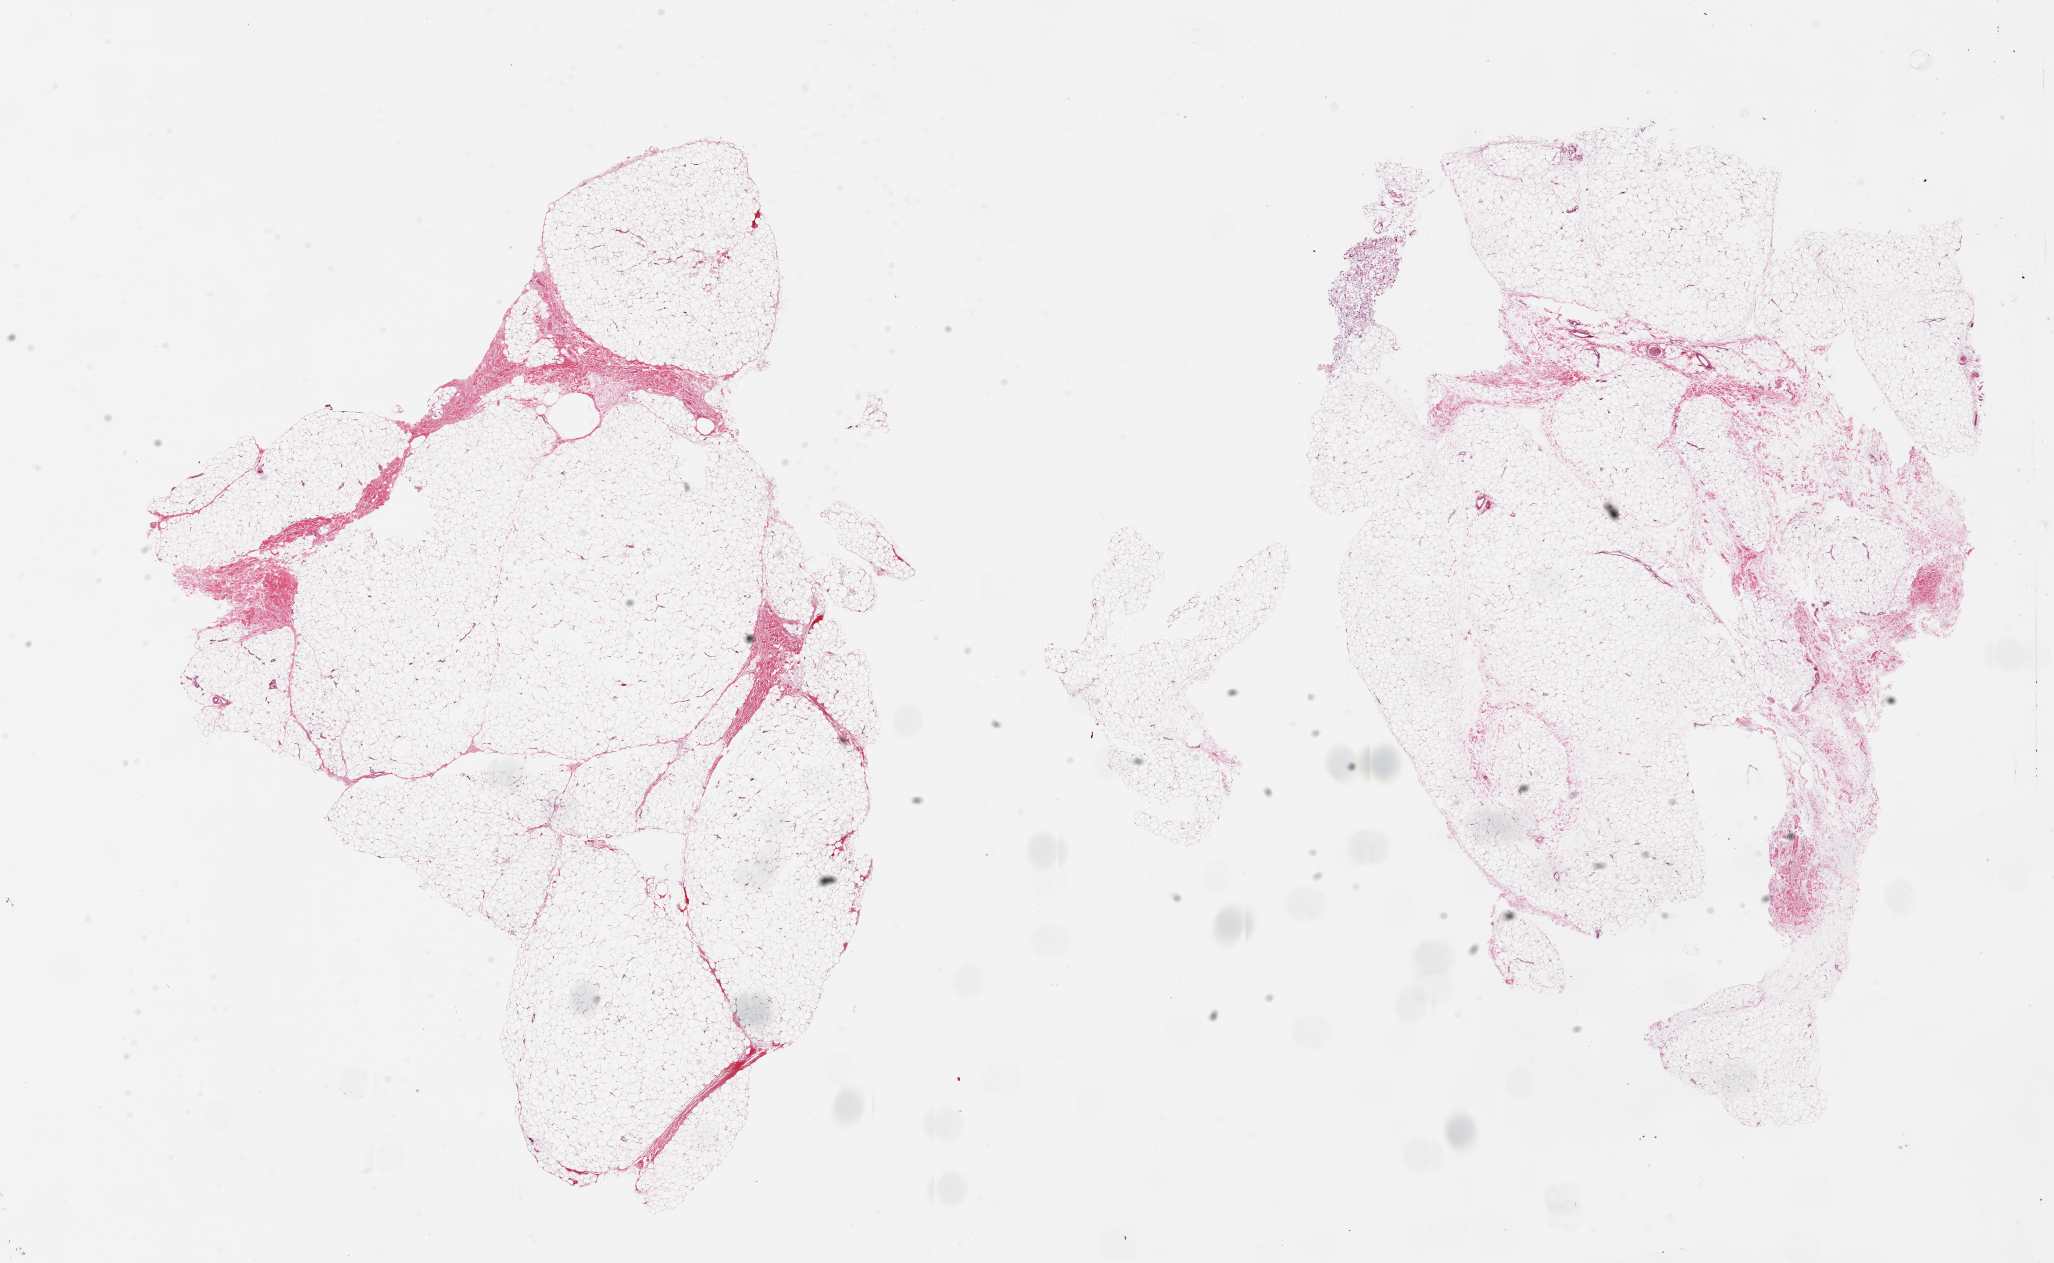
H&E whole-slide image, brightfield, whole scanned area (about 32.5 x 20.0 mm, acquisition: 20x scan) shown as a low-resolution overview. PAXgene-fixed paraffin-embedded (PFPE) section. Sampled site (target tissue): adipose tissue. Tissue donor sample. Donor: female.
Review note (as recorded): 2 pieces, 17x12 & 17x16mm.